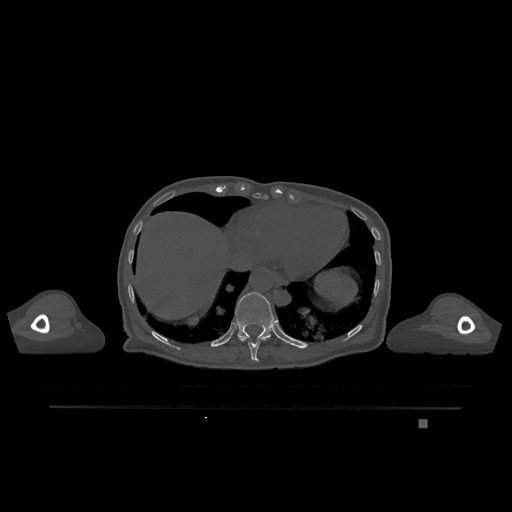
CT including the spine, one axial slice; position 613 of 1317 along the scan axis; bone window (W 1800 / L 400 HU); 0.5 mm slice thickness; 512 × 512 image matrix. Patient: female, 74 years. Case-level facts recorded for this patient, not image findings: primary cancer: lung; vertebrae with lytic lesions (as recorded): T1, T4, T5, T6, L4, L5.
Outlined on this slice (semi-automatically segmented with operator editing):
- T10 vertebra: bounding box [x1, y1, x2, y2] px = [238, 337, 270, 361]
- T11 vertebra: [229, 292, 276, 341]